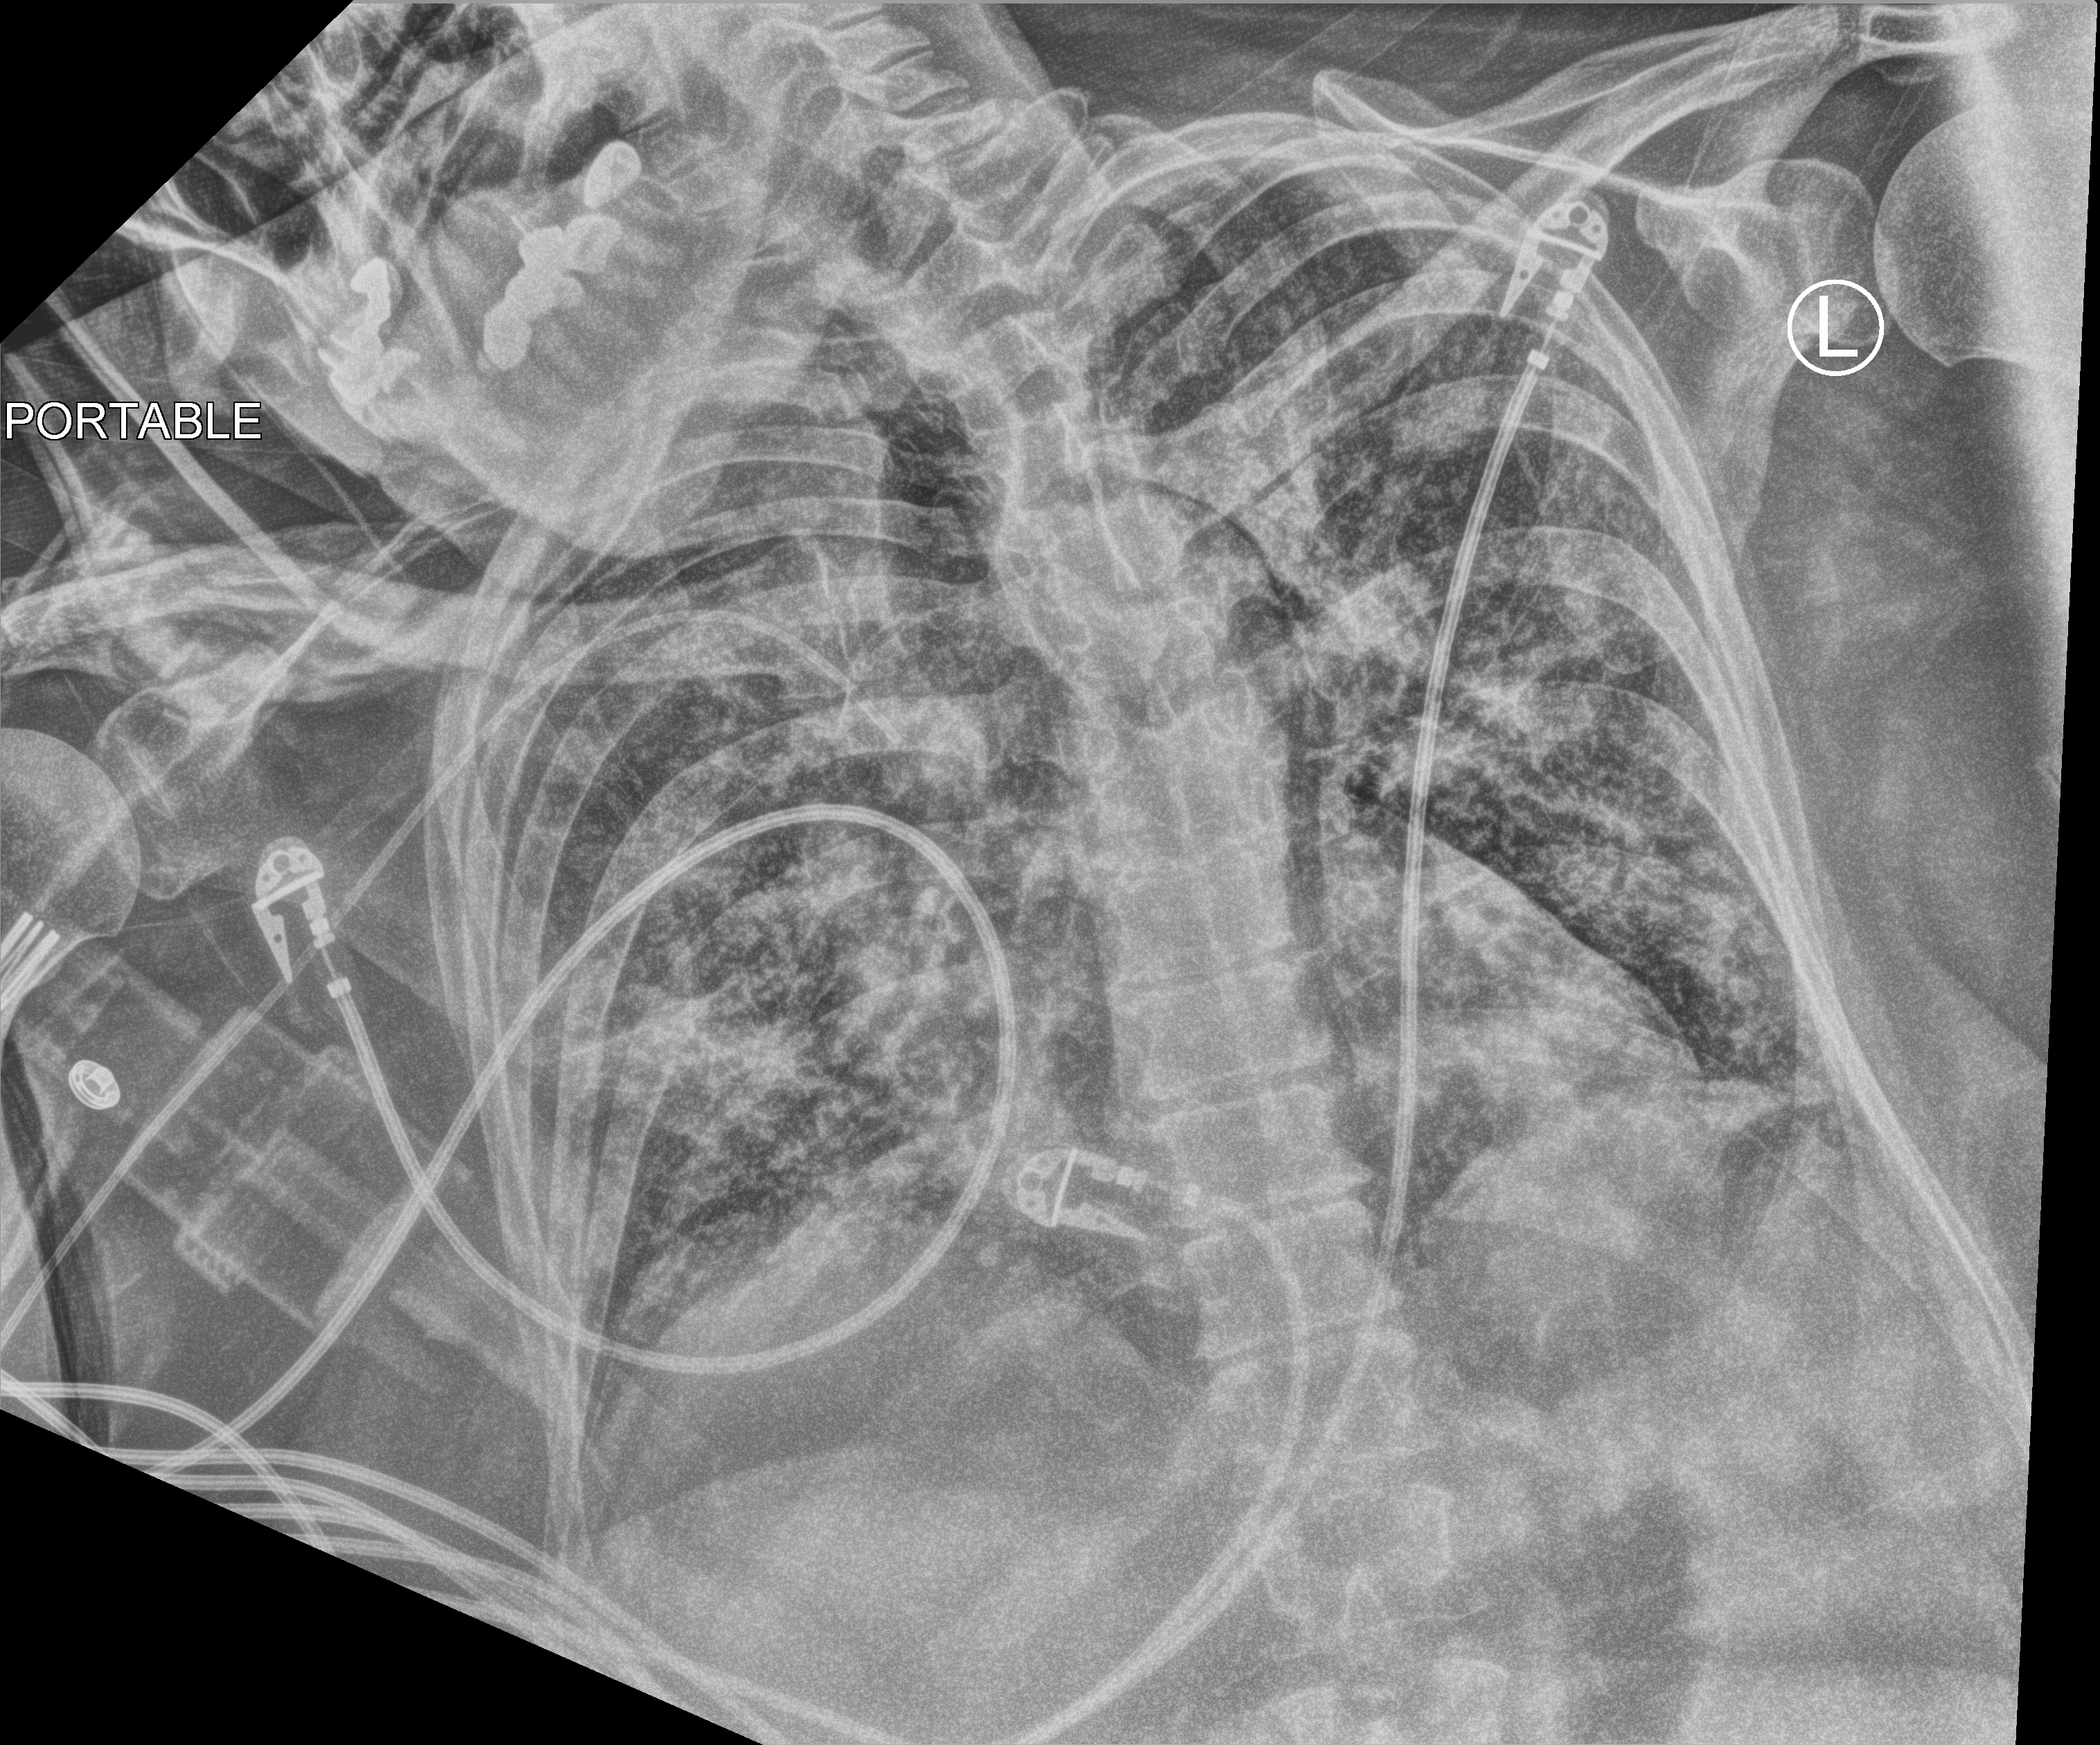
Portable chest radiograph, anteroposterior (AP) projection. Patient hospitalised with COVID-19; female, aged 60–74 years.
Hospital-stay facts (about this admission, not read from this image; timing relative to this image not recorded): diabetes (admission record): no.